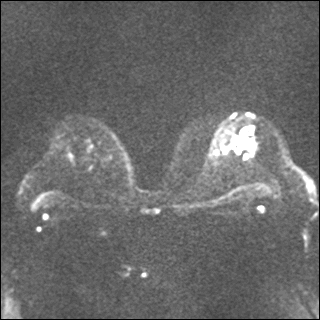
Breast MRI, one axial slice. Slice 20 of 35 in the series (ordered by position). Diffusion-weighted series; image 2 of 4 stored at this slice position (different b-values; order by instance number). 1.5 T. 4 mm slice thickness. 320 × 320 image matrix. Female patient.
Structures marked on this image (outlined manually by an expert reader):
- tumour on diffusion-weighted imaging: bounding box (x1, y1, x2, y2) in pixels: (240, 145, 244, 148)